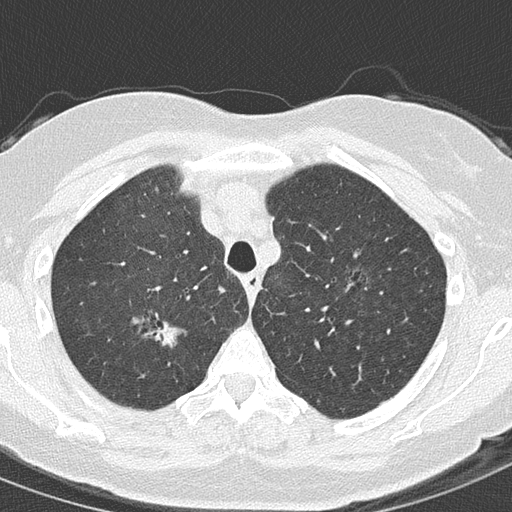
Low-dose screening chest CT, axial slice. Second annual screen. Lung window (W 1500 / L -600 HU). 2 mm slice thickness. Slice 38 of 157 in the series. 512 × 512 image matrix. Female participant, aged 61 years at enrolment. Current smoker at enrolment.
Lesion marked by an expert reader, bounding box (x1, y1, x2, y2) in pixels: (145, 310, 187, 349). Screening reader's record for this exam (one nodule recorded; not confirmed to be the boxed lesion): non-calcified nodule or mass ≥4 mm, right upper lobe, 15 × 10 mm, spiculated (stellate) margins, ground glass attenuation, pre-existing on the prior screen: yes; interval growth: yes. Official screen result: positive, other.